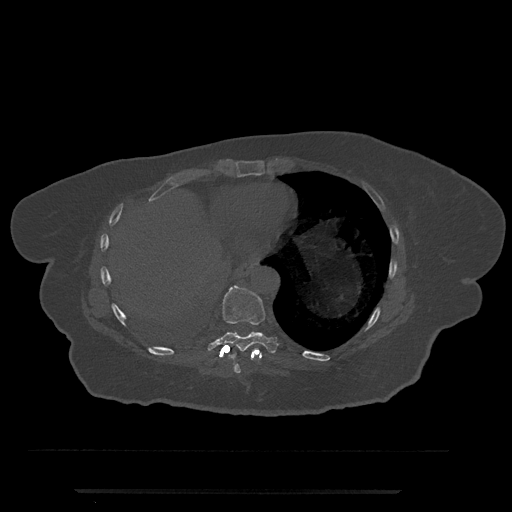
CT including the spine, one axial slice. 120 kVp. Bone window (W 1800 / L 400 HU). 512 × 512 image matrix, field of view 440 × 440 mm. Patient: female, 51 years. From the clinical record (not read from this slice): primary cancer: neuro; vertebrae with lytic lesions (as recorded): T8.
Structures marked on this image (semi-automatic segmentation, software-assisted and operator-edited):
- T8 vertebra: box from (x=233, y=353) to (x=241, y=373) px
- T9 vertebra: (x=207, y=286)–(x=279, y=358)